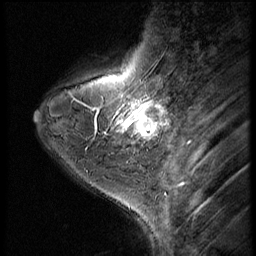
Breast MRI (dynamic contrast-enhanced), one sagittal slice; slice 16 of 56 in the series (ordered by position); dynamic contrast-enhanced series, image 2 of 3 at this slice position (ordered by acquisition); 1.5 T; TE 4.2 ms, TR 9 ms; 2.5 mm slice thickness; 256 × 256 image matrix, field of view 180 × 180 mm. Female patient, age 38 years. From the clinical record (not read from this slice): setting: breast cancer imaged before/during neoadjuvant chemotherapy; receptor status: triple-negative.
Annotated regions visible in this slice (semi-automatic segmentation, software-assisted and operator-edited):
- analysis volume of interest (the breast-tissue region the enhancement analysis was run in; not a lesion): bounding box [x1, y1, x2, y2] px = [107, 95, 179, 149]
- tumour enhancement mask (voxels above the 140 % enhancement threshold inside the analysis volume of interest): [115, 101, 162, 137]